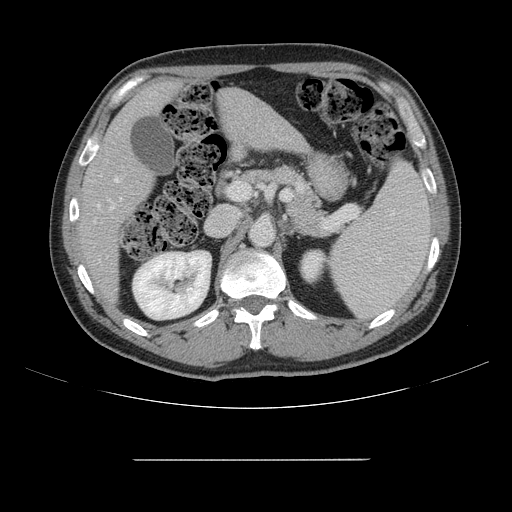
Contrast-enhanced abdominal CT, one axial slice. Slice 83 of 164 in the series (ordered by position). 120 kVp. Intravenous contrast given. Soft-tissue window (W 400 / L 40 HU). 2.5 mm slice thickness. 512 × 512 image matrix, field of view 404 × 404 mm. Male patient, age 54 years. From the clinical record (not read from this slice): diagnosis: colorectal cancer liver metastases, imaged before liver resection; multiple liver metastases: yes; largest metastasis: 1 cm; chemotherapy before resection: yes.
Structures marked on this image (manually delineated by an expert):
- hepatic veins: bounding box (x1, y1, x2, y2) in pixels: (97, 177, 118, 261)
- liver: (82, 83, 304, 296)
- planned liver remnant (the part of the liver to remain after resection): (82, 83, 225, 297)
- portal vein (with intrahepatic branches): (110, 198, 121, 210)